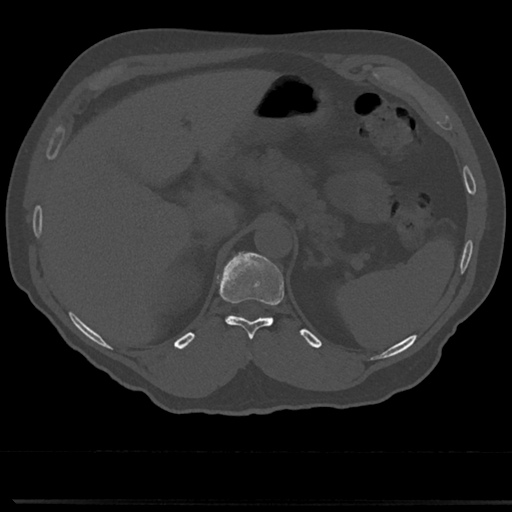
CT including the spine, one axial slice; position 193 of 817 along the scan axis; reconstruction kernel Br40s/3; 120 kVp; bone window (W 1800 / L 400 HU); 0.5 mm slice thickness; 512 × 512 image matrix, field of view 355 × 355 mm. Patient: male, 61 years. From the clinical record (not read from this slice): primary cancer: prostate.
Structures marked on this image (semi-automatically segmented with operator editing):
- T11 vertebra: bounding box [x1, y1, x2, y2] px = [221, 257, 284, 341]
- T12 vertebra: [243, 253, 256, 260]